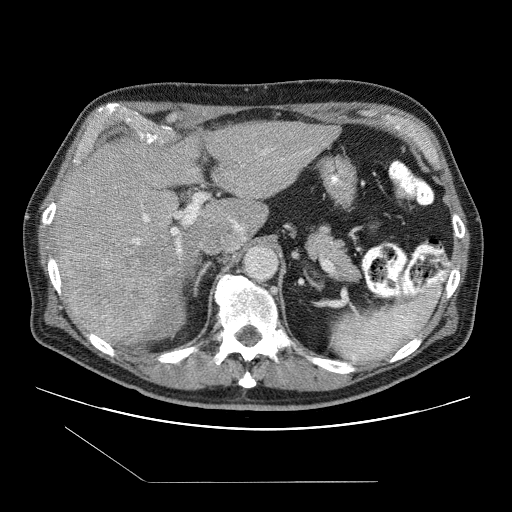
Contrast-enhanced abdominal CT (liver protocol), one axial slice. Position 64 of 109 along the scan axis. 120 kVp. One of 2 acquisitions stored at this slice position. Soft-tissue window (W 400 / L 40 HU). 512 × 512 image matrix, field of view 400 × 400 mm. From the clinical record (not read from this slice): diagnosis: hepatocellular carcinoma (patient treated with transarterial chemoembolisation; whether this scan precedes or follows treatment is not stated here); TNM stage (as recorded): Stage-IIIB; Child-Pugh class: A; tumour differentiation: well differentiated; tumour nodularity: multinodular.
Structures marked on this image (semi-automatic segmentation, software-assisted and operator-edited):
- abdominal aorta: box from (x=245, y=246) to (x=277, y=278) px
- liver parenchyma outside the tumour (the mass and vessels are separate outlines, so this box may not span the whole liver): (x=52, y=122)–(x=338, y=338)
- mass: (x=58, y=247)–(x=162, y=344)
- liver vessels: (x=132, y=151)–(x=309, y=253)